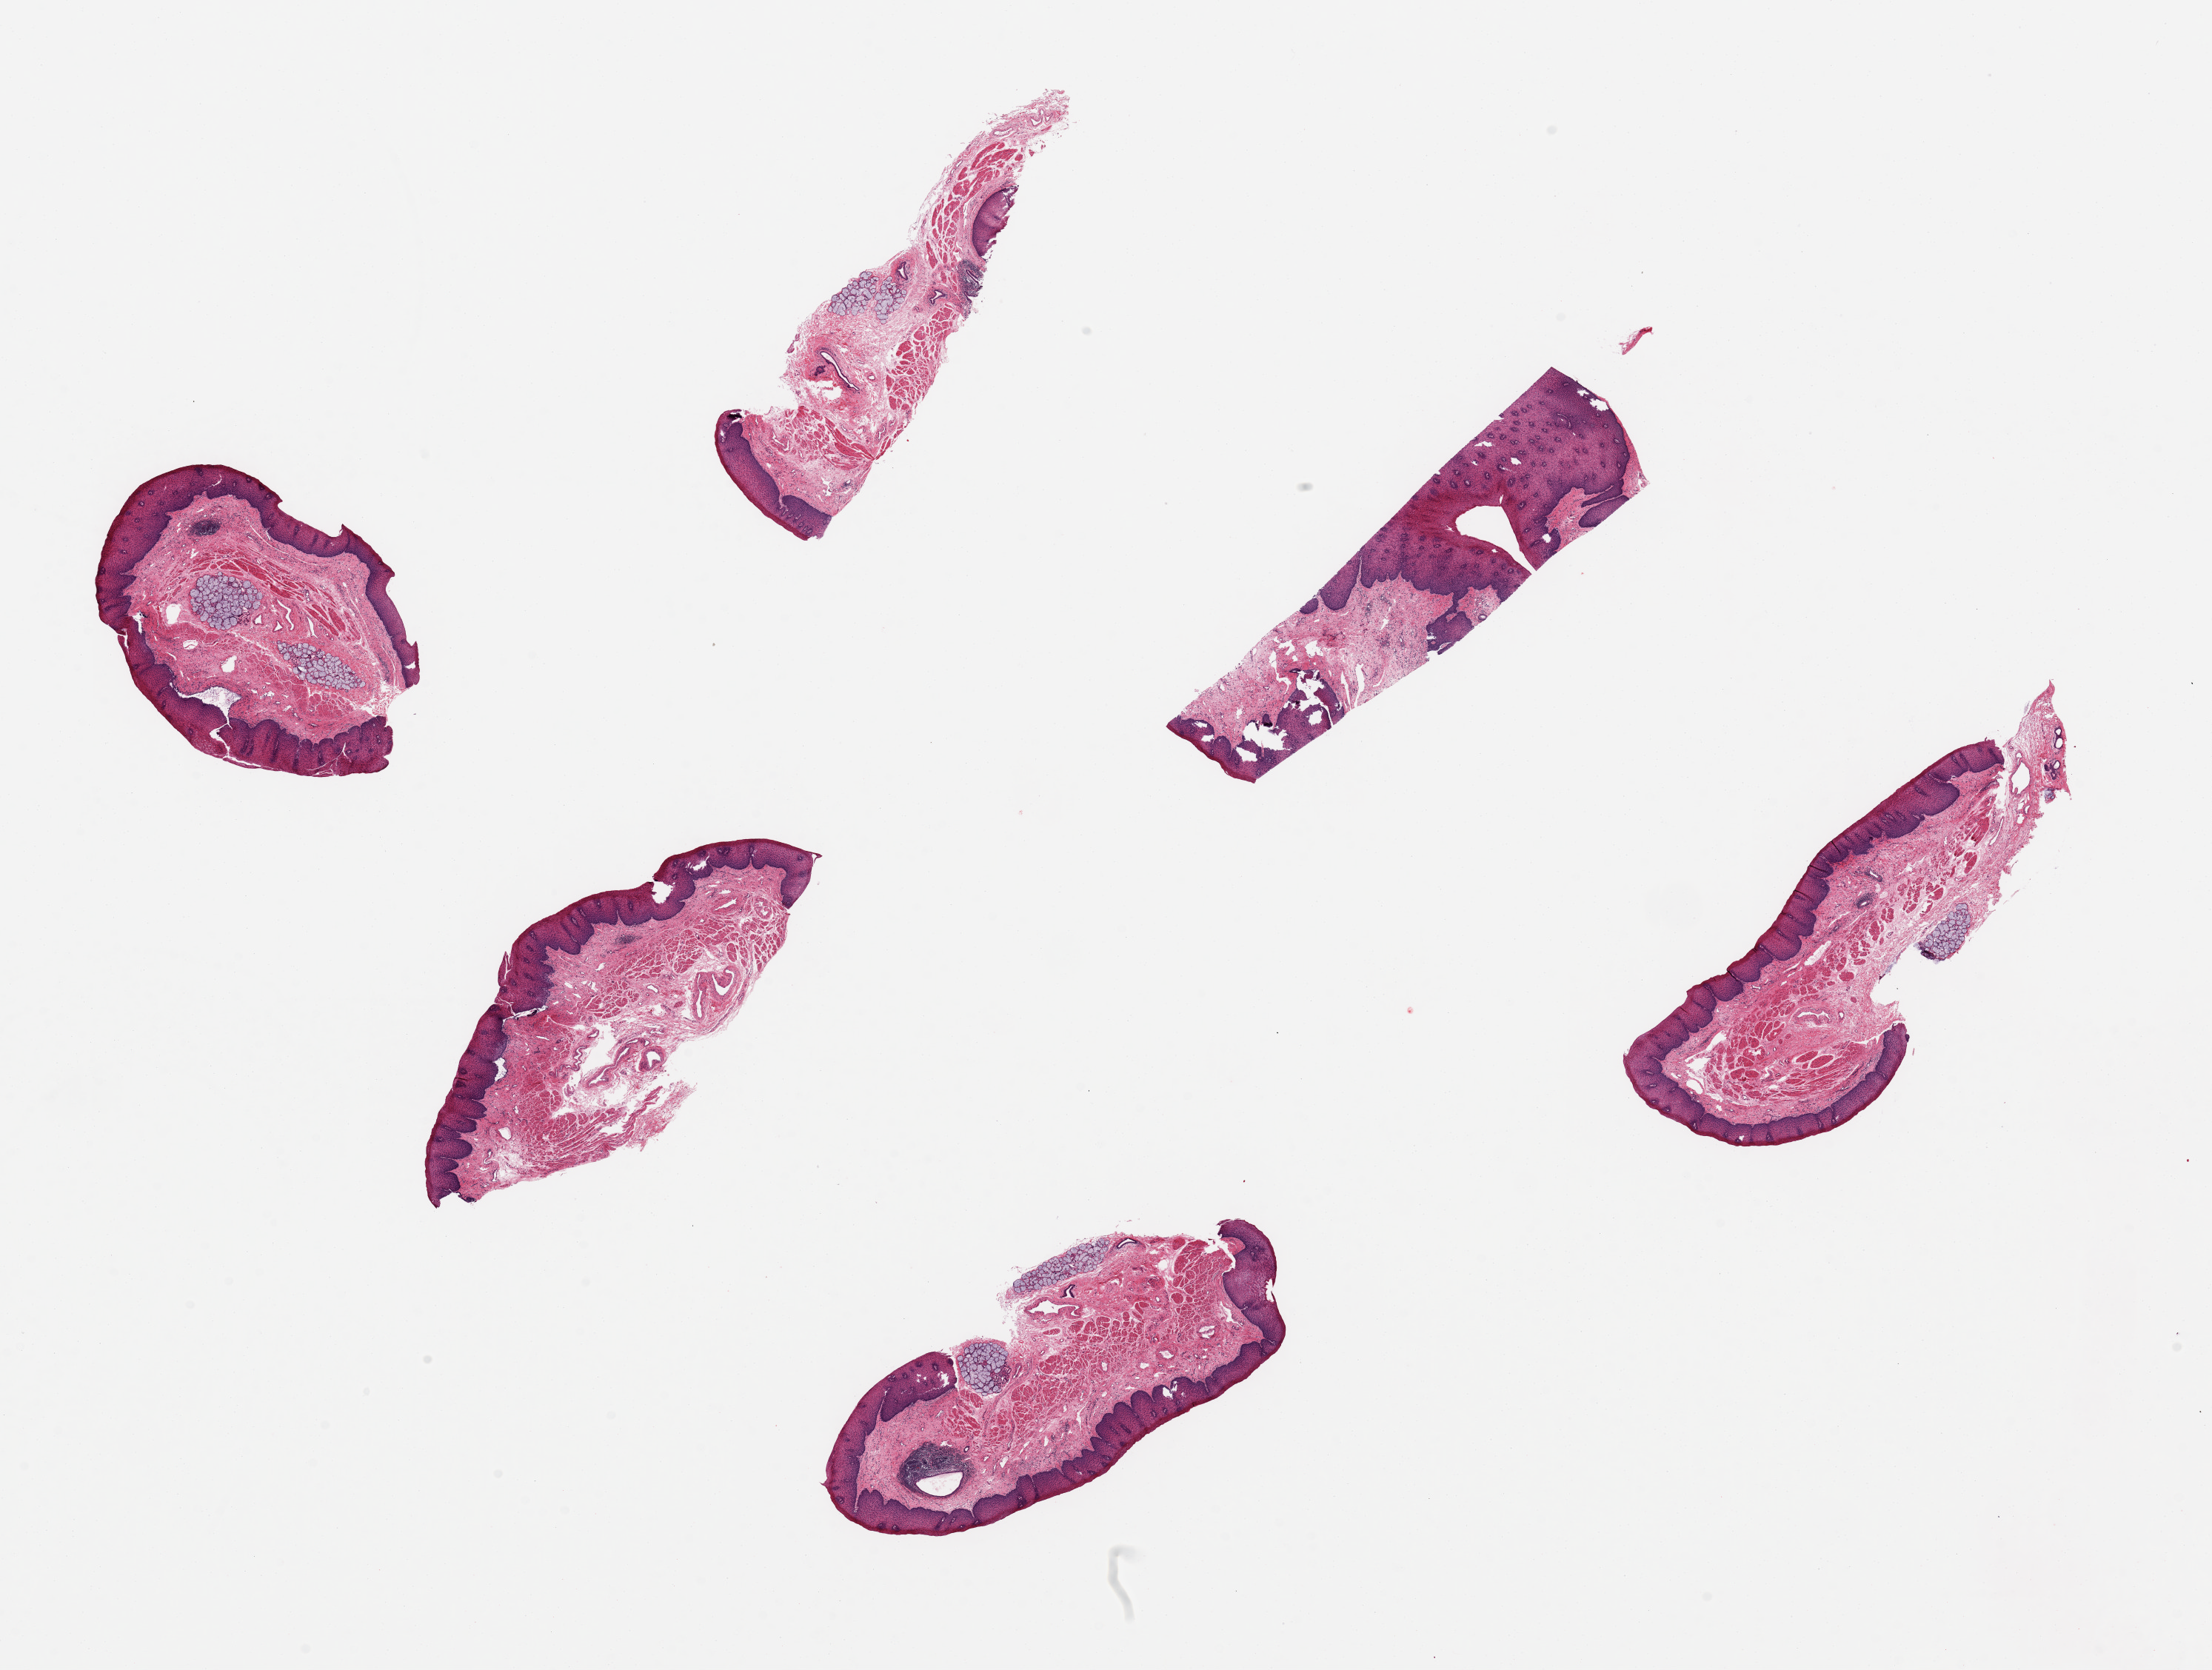
Whole-slide image, haematoxylin and eosin stain, a low-resolution overview of the entire scanned area, about 23.6 x 17.8 mm, PAXgene-fixed, paraffin-embedded tissue, target tissue: esophageal mucous membrane, tissue donor sample. Female donor.
* review note (as recorded): 6 pieces, ~6x2mm. Squamous mucosa is ~20% of thickness